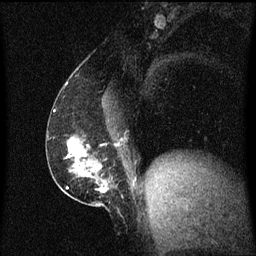
Breast MRI (dynamic contrast-enhanced), one sagittal slice. Slice 29 of 60 in the series (ordered by position). Dynamic contrast-enhanced series, image 2 of 3 at this slice position (ordered by acquisition). 1.5 T. TE 4.2 ms, TR 8.4 ms. 2 mm slice thickness. 256 × 256 image matrix. Patient: female, 52 years. Case-level facts recorded for this patient, not image findings: setting: breast cancer imaged before/during neoadjuvant chemotherapy; receptor status: HER2-positive.
Outlined on this slice (semi-automatic segmentation, software-assisted and operator-edited):
- analysis volume of interest (the breast-tissue region the enhancement analysis was run in; not a lesion): bounding box [x1, y1, x2, y2] px = [62, 136, 117, 203]
- tumour enhancement mask (voxels above the 70 % enhancement threshold inside the analysis volume of interest): [69, 138, 107, 193]